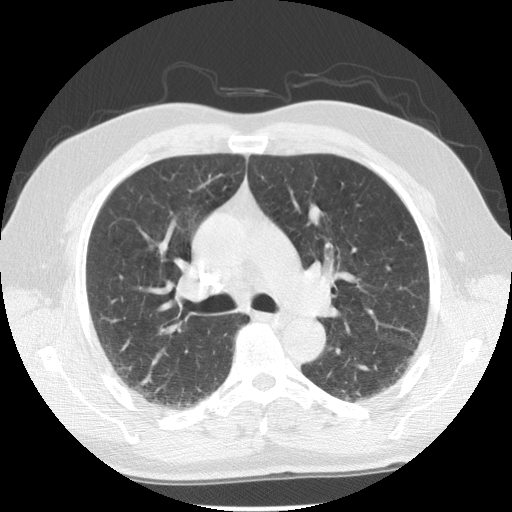
Chest CT (low-dose screening protocol), one axial image; first (baseline) screen; lung window (W 1500 / L -600 HU); 2.5 mm slice thickness; 140 kVp; slice 77 of 124 in the series. Male participant, aged 59 years at enrolment. Current smoker at enrolment.
Expert reader's lesion annotation, bounding box (x1, y1, x2, y2) in pixels: (127, 221, 172, 263). Screening reader's record for this exam: no non-calcified nodule ≥4 mm recorded. Official screen result: negative screen, minor abnormalities not suspicious for lung cancer. Later outcome: lung cancer diagnosed 659 days after this screen — large cell carcinoma, NOS, right upper lobe, poorly differentiated (G3), stage IIIA (AJCC 6th edition), 34 mm at pathology.